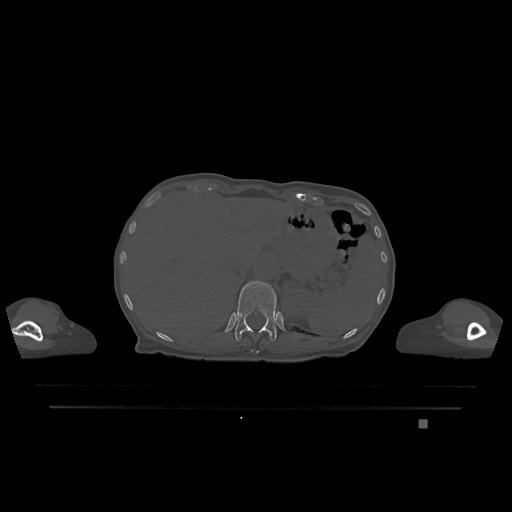
CT including the spine, one axial slice; slice 544 of 1317 in the series (ordered by position); bone window (W 1800 / L 400 HU); 0.5 mm slice thickness; 512 × 512 image matrix, field of view 500 × 500 mm. Female patient, age 74 years. Case-level facts recorded for this patient, not image findings: primary cancer: lung.
Annotated regions visible in this slice (semi-automatic segmentation, software-assisted and operator-edited):
- T11 vertebra: box from (x=251, y=351) to (x=259, y=353) px
- T12 vertebra: (x=235, y=281)–(x=277, y=341)